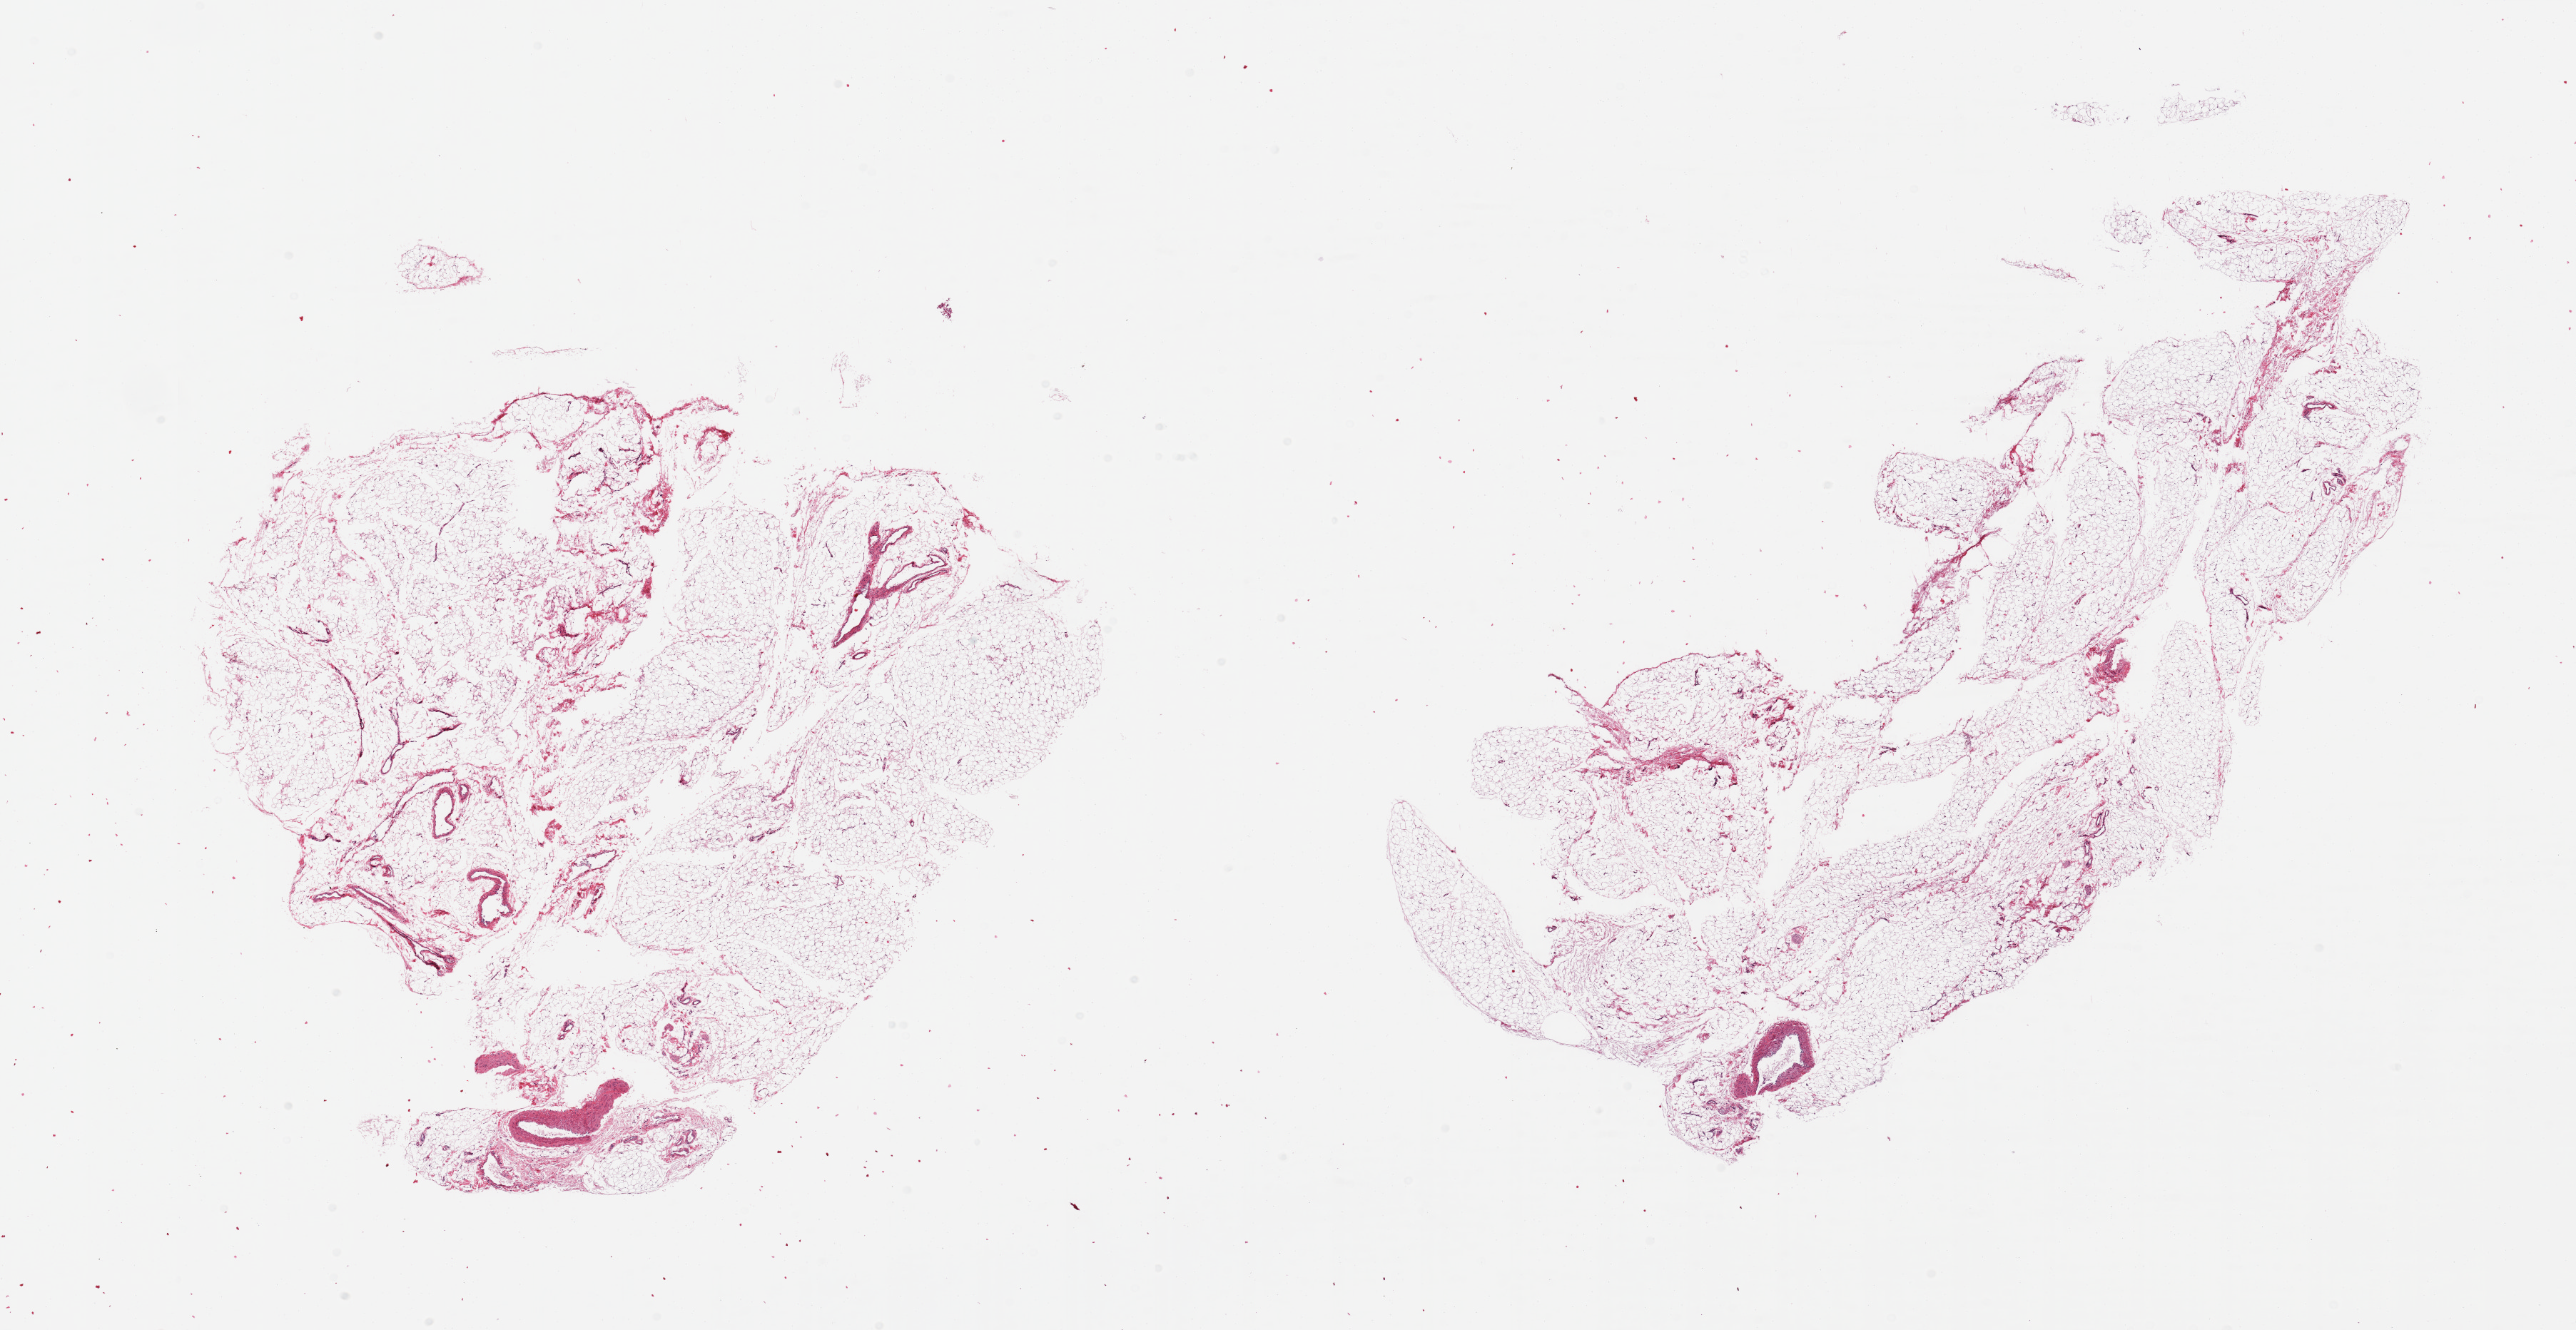
Hematoxylin and eosin (H&E) whole-slide image — shown as a low-resolution overview of the whole scanned area (about 28.5 x 14.7 mm). PAXgene-fixed, paraffin-embedded tissue. Target tissue: omentum. Tissue donor sample. Donor: female.
* pathologist's review note for this sample: 2 pieces, ~5% vascular elements